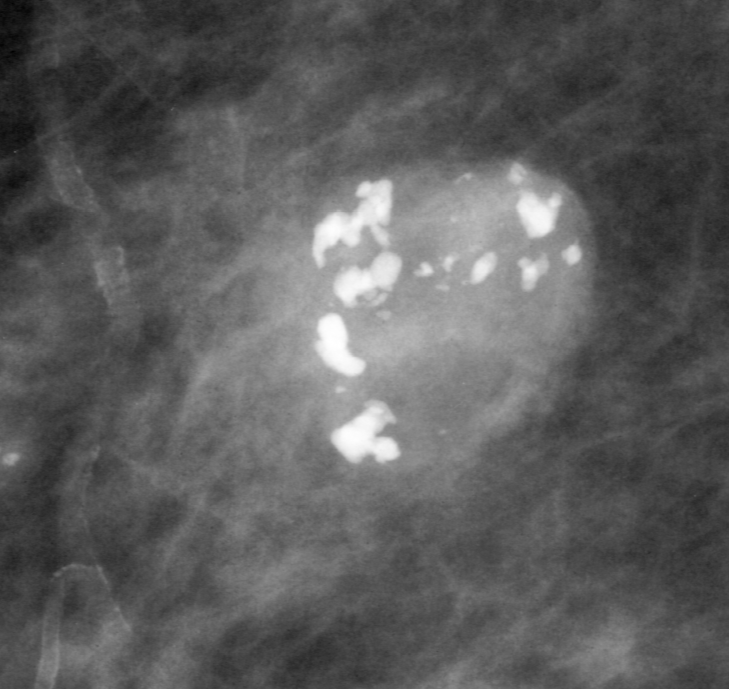
Region of interest cut from a scanned film mammogram (one marked finding); left breast; MLO view; BI-RADS breast density category 3 (scale 1–4).
- Finding: calcifications, morphology amorphous; BI-RADS assessment category 2; subtlety rating 5 on a 1 (subtle) to 5 (obvious) scale; pathology (as recorded): benign.